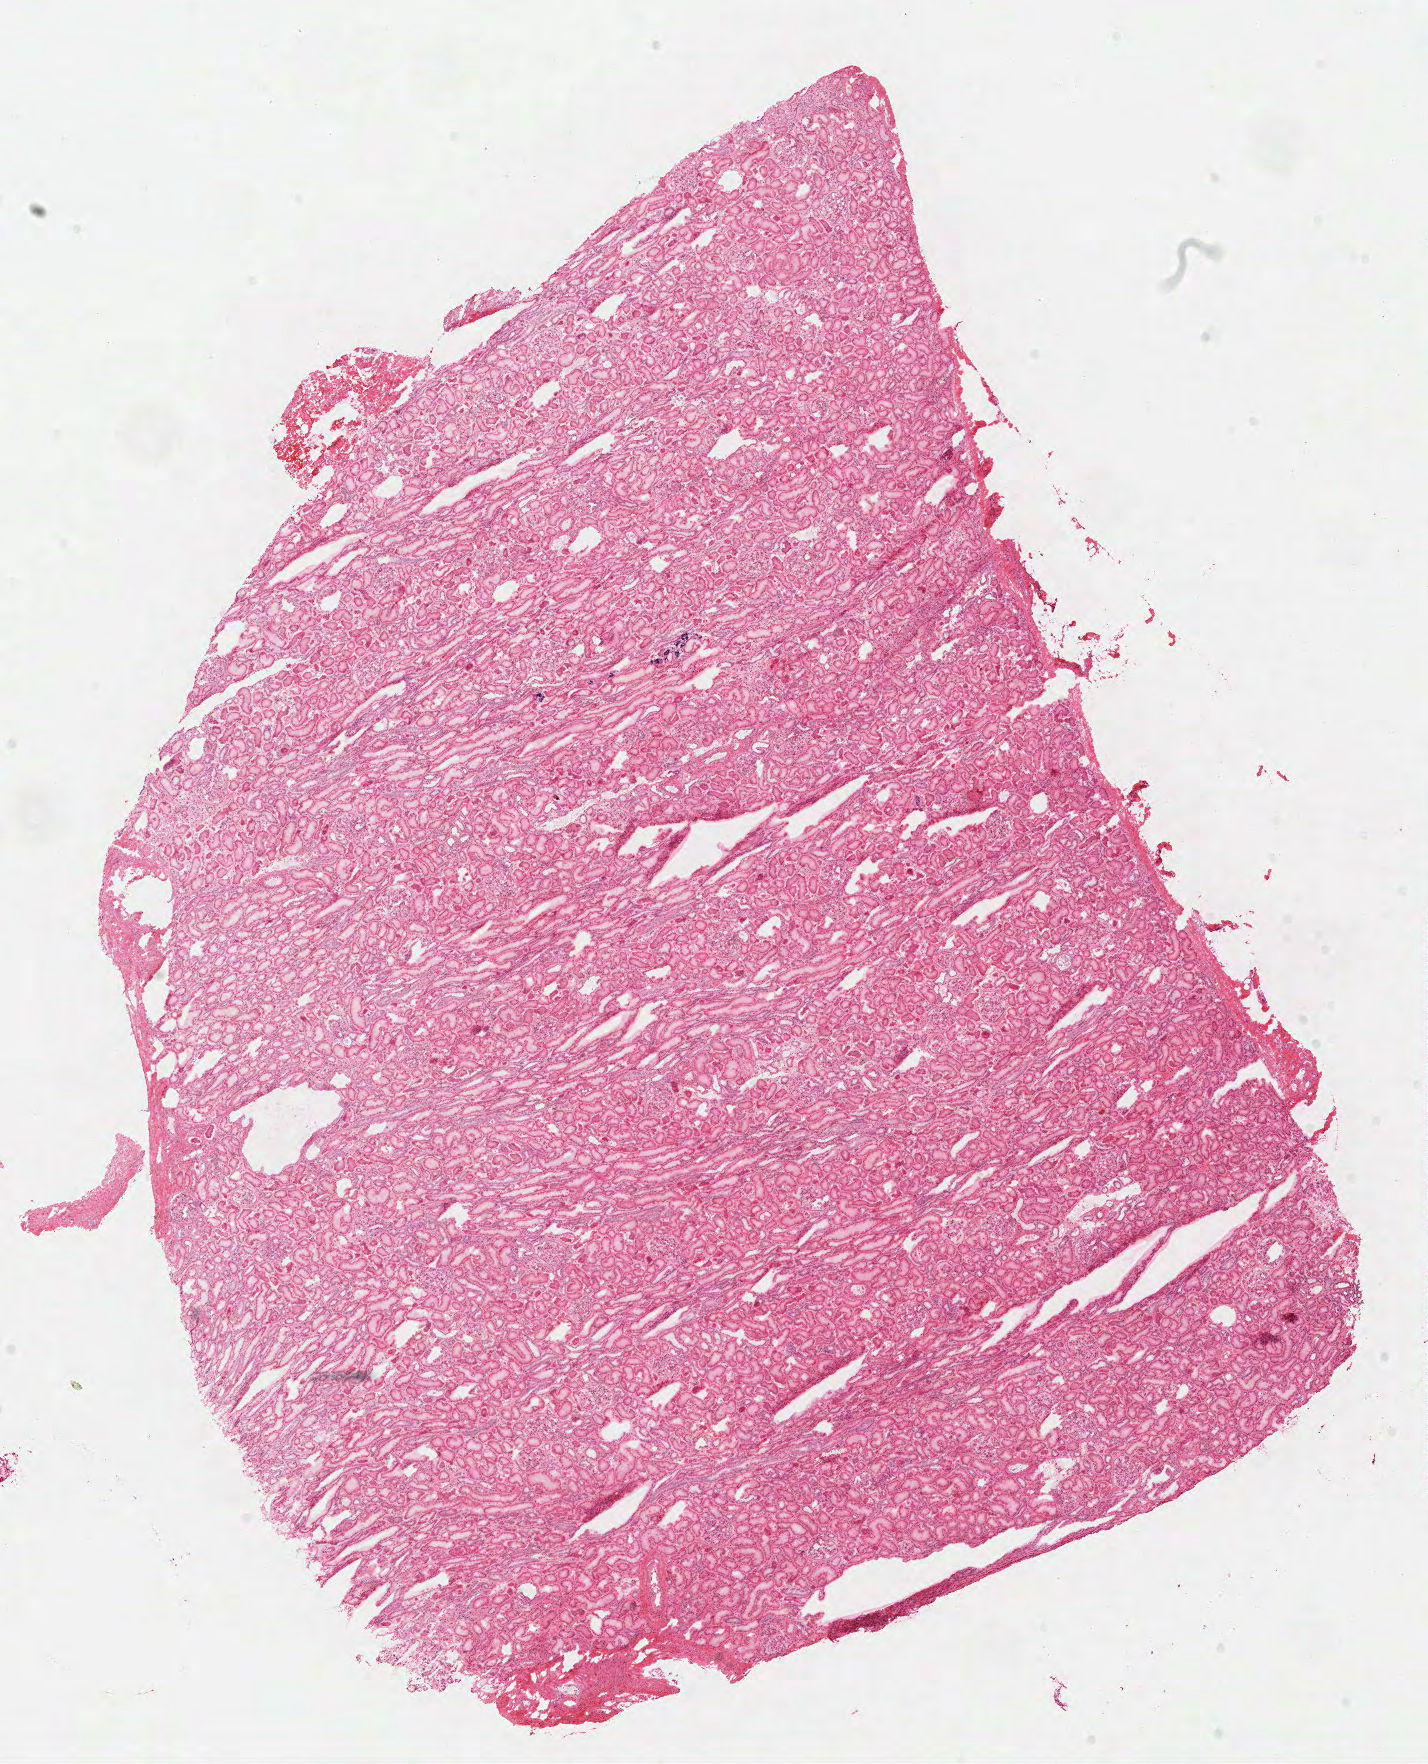
Hematoxylin and eosin (H&E) stained whole-slide image — low-resolution overview of the scanned area, about 11.3 x 13.9 mm. Frozen section from the top of the tissue portion. Solid tissue normal (non-tumour tissue) sample from the kidney. Male patient; age at initial diagnosis 54 years.
This section: solid tissue normal (non-tumour) sample from the same patient. Patient diagnosis: Papillary adenocarcinoma, NOS.